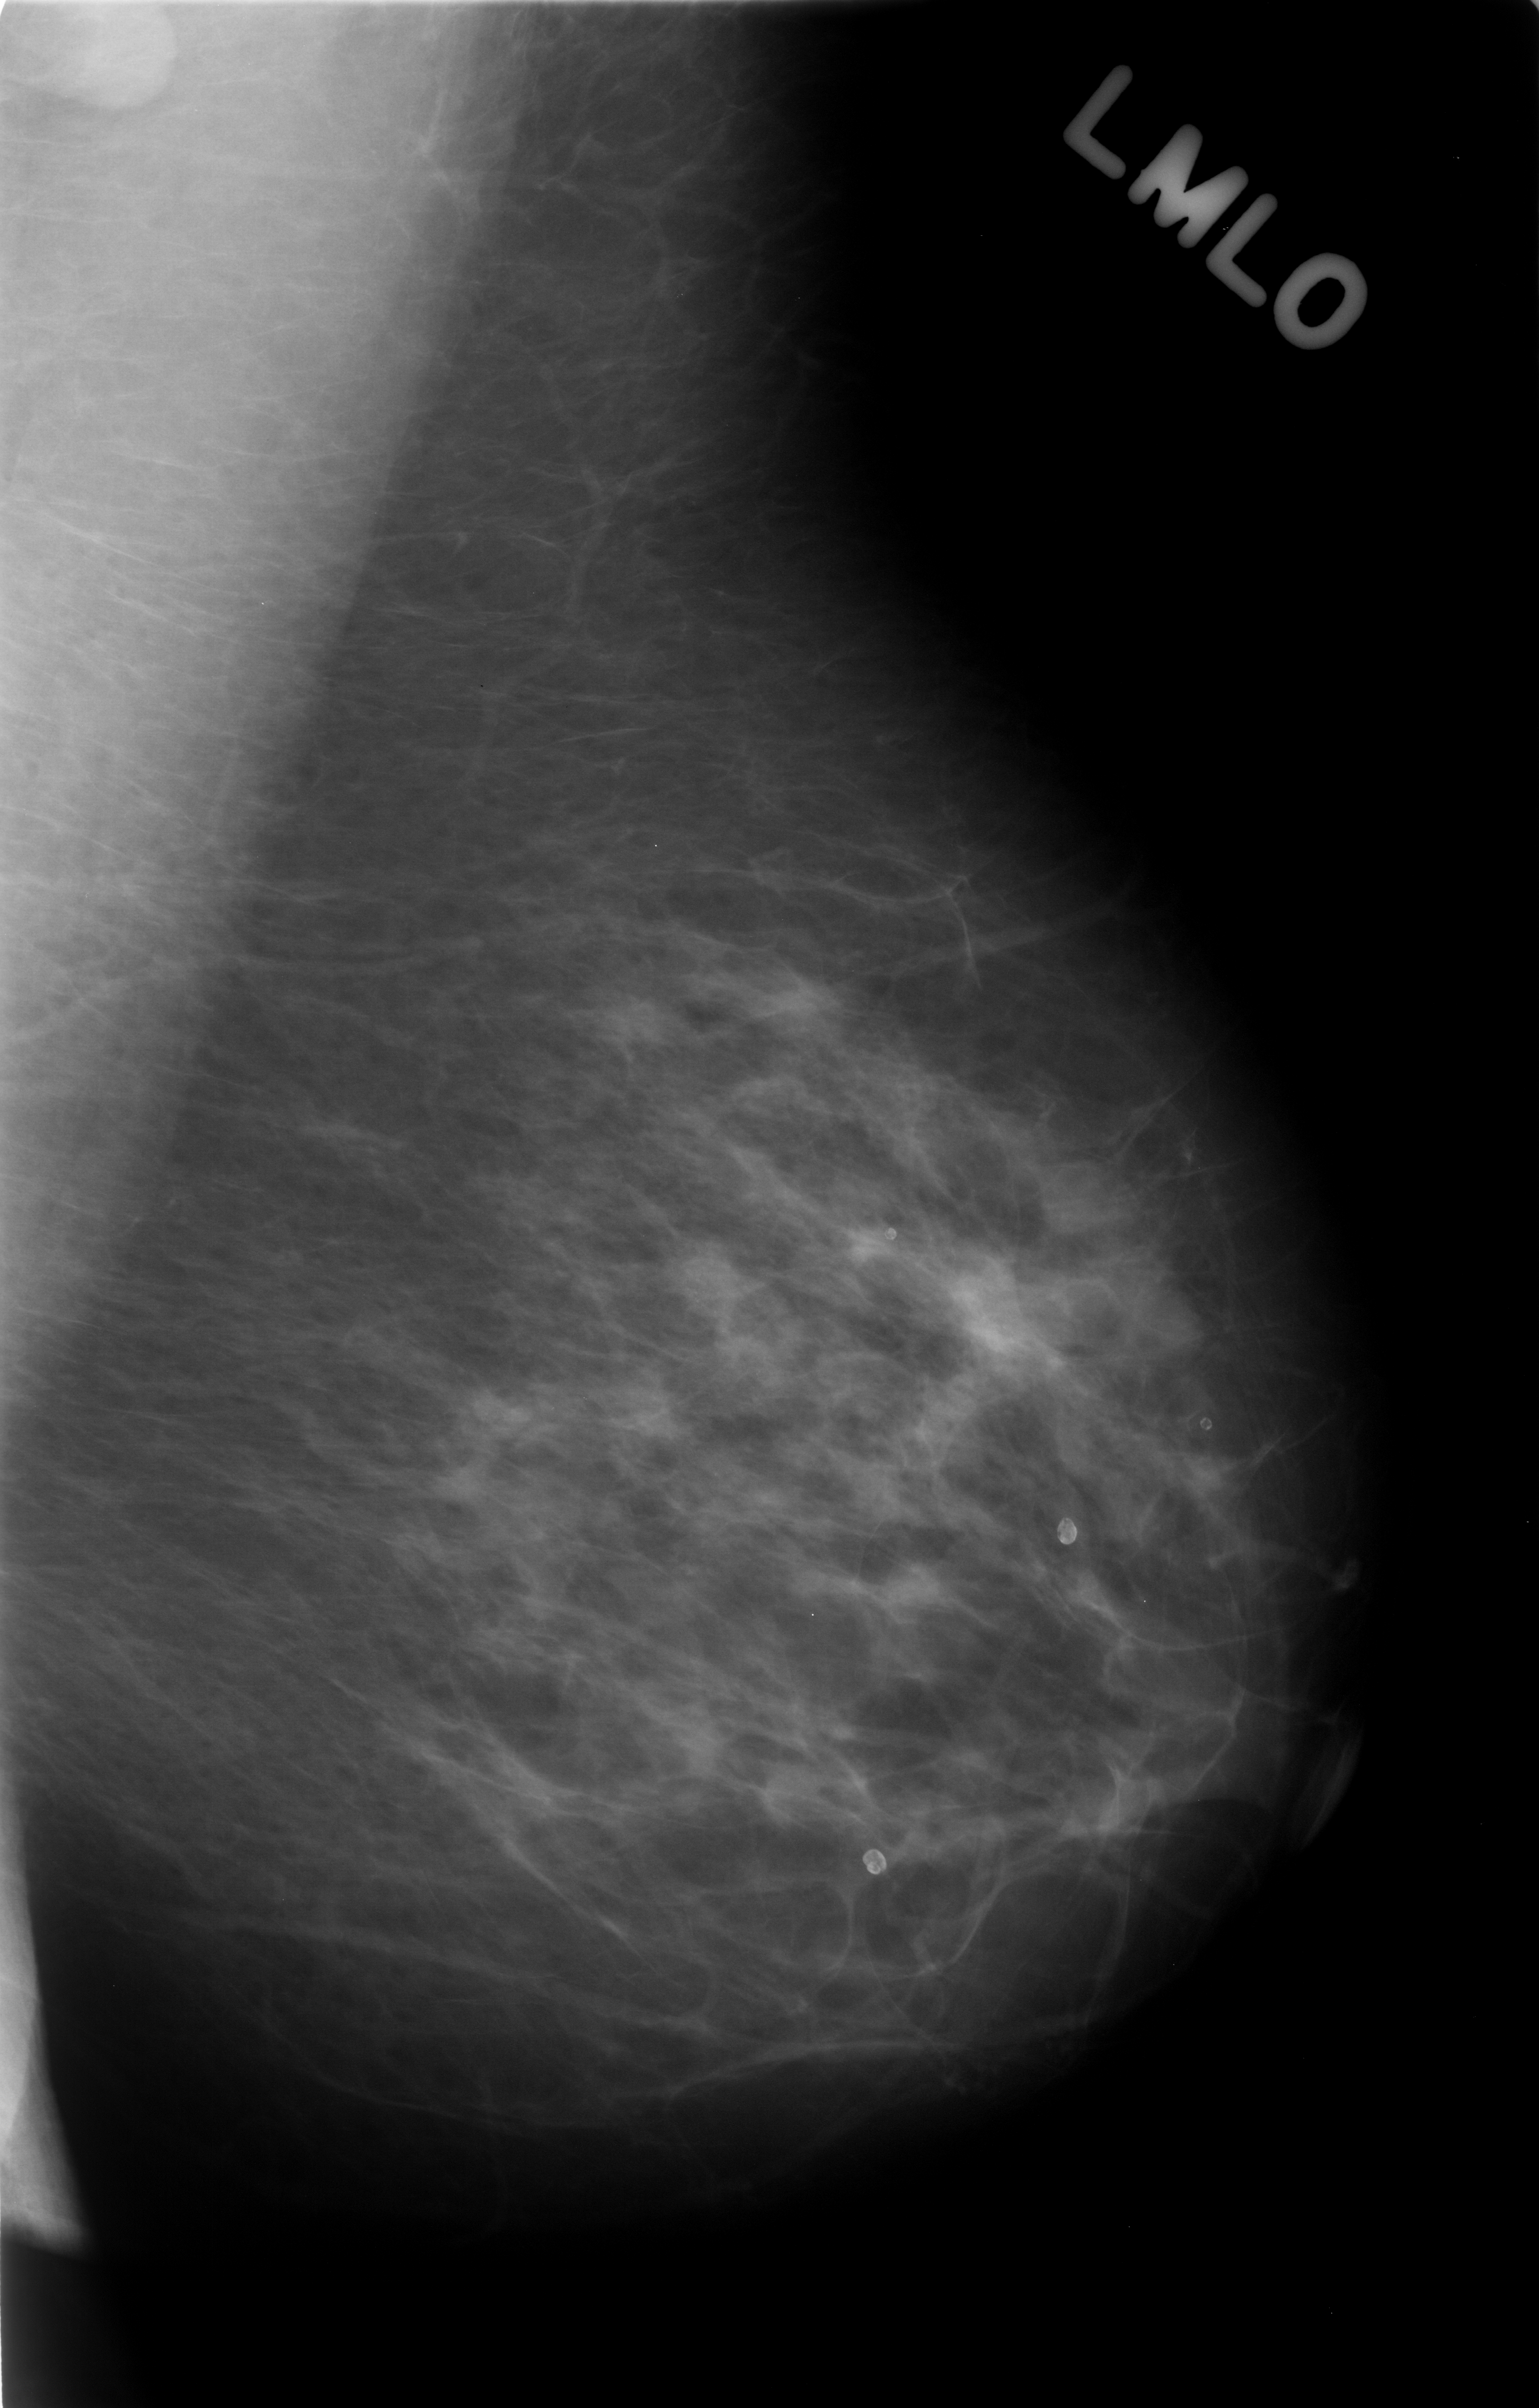
Scanned film-screen mammogram. Left breast. MLO view. BI-RADS breast density category 2 (scale 1–4). 1539 × 2408 image matrix.
Marked abnormalities (boxes around the expert regions of interest):
- calcifications, morphology amorphous, distribution clustered; BI-RADS assessment category 4; subtlety rating 1 on a 1 (subtle) to 5 (obvious) scale; pathology (as recorded): benign: bounding box <631,1208,777,1353> (left, top, right, bottom; pixels)